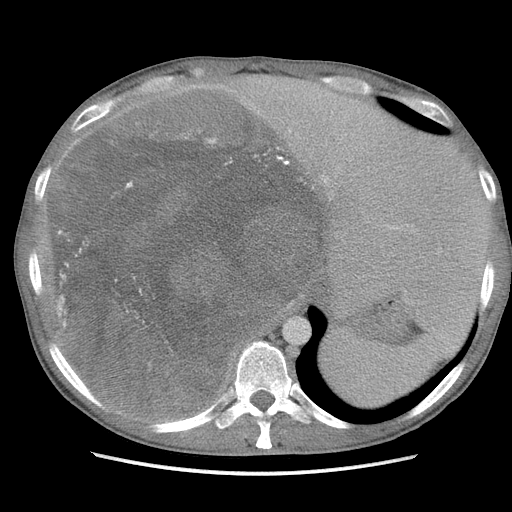
Contrast-enhanced abdominal CT, one axial slice. Position 84 of 115 along the scan axis. Soft-tissue window (W 400 / L 40 HU). 5 mm slice thickness. 512 × 512 image matrix, field of view 360 × 360 mm. Male patient. Case-level facts recorded for this patient, not image findings: diagnosis: adrenocortical carcinoma; tumour side: right adrenal.
Structures marked on this image (semi-automatic segmentation, software-assisted and operator-edited):
- mass: bounding box (x1, y1, x2, y2) in pixels: (55, 89, 315, 415)